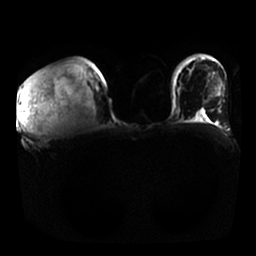
Breast MRI, one axial slice; slice 13 of 25 in the series (ordered by position); diffusion-weighted series; image 2 of 4 stored at this slice position (different b-values; order by instance number); 1.5 T; 4 mm slice thickness; 256 × 256 image matrix, field of view 350 × 350 mm. Female patient.
Structures marked on this image (manually delineated by an expert):
- tumour on diffusion-weighted imaging: box from (x=17, y=71) to (x=56, y=133) px